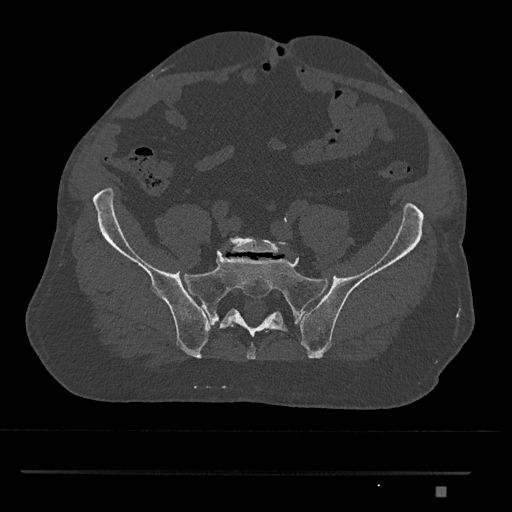
CT including the spine, one axial slice; position 499 of 1134 along the scan axis; reconstruction kernel Br40s/3; 120 kVp; bone window (W 1800 / L 400 HU); 512 × 512 image matrix. Male patient, age 65 years. Case-level facts recorded for this patient, not image findings: primary cancer: prostate.
Annotated regions visible in this slice (semi-automatic segmentation, software-assisted and operator-edited):
- L5 vertebra: bounding box <228,236,289,254> (left, top, right, bottom; pixels)